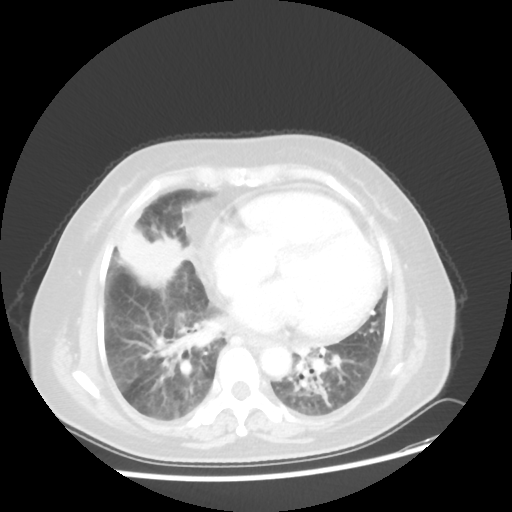
Chest CT, one axial slice. Reconstruction kernel STANDARD. 100 kVp. Lung window (W 1500 / L -600 HU). 5 mm slice thickness. 512 × 512 image matrix, field of view 359 × 359 mm. Patient: female, 67 years. From the clinical record (not read from this slice): clinical TNM (as recorded): T2a N3 M1a.
Outlined on this slice (bounding box drawn by a radiologist):
- lung tumour (recorded histology: adenocarcinoma): bounding box [x1, y1, x2, y2] px = [117, 224, 181, 288]